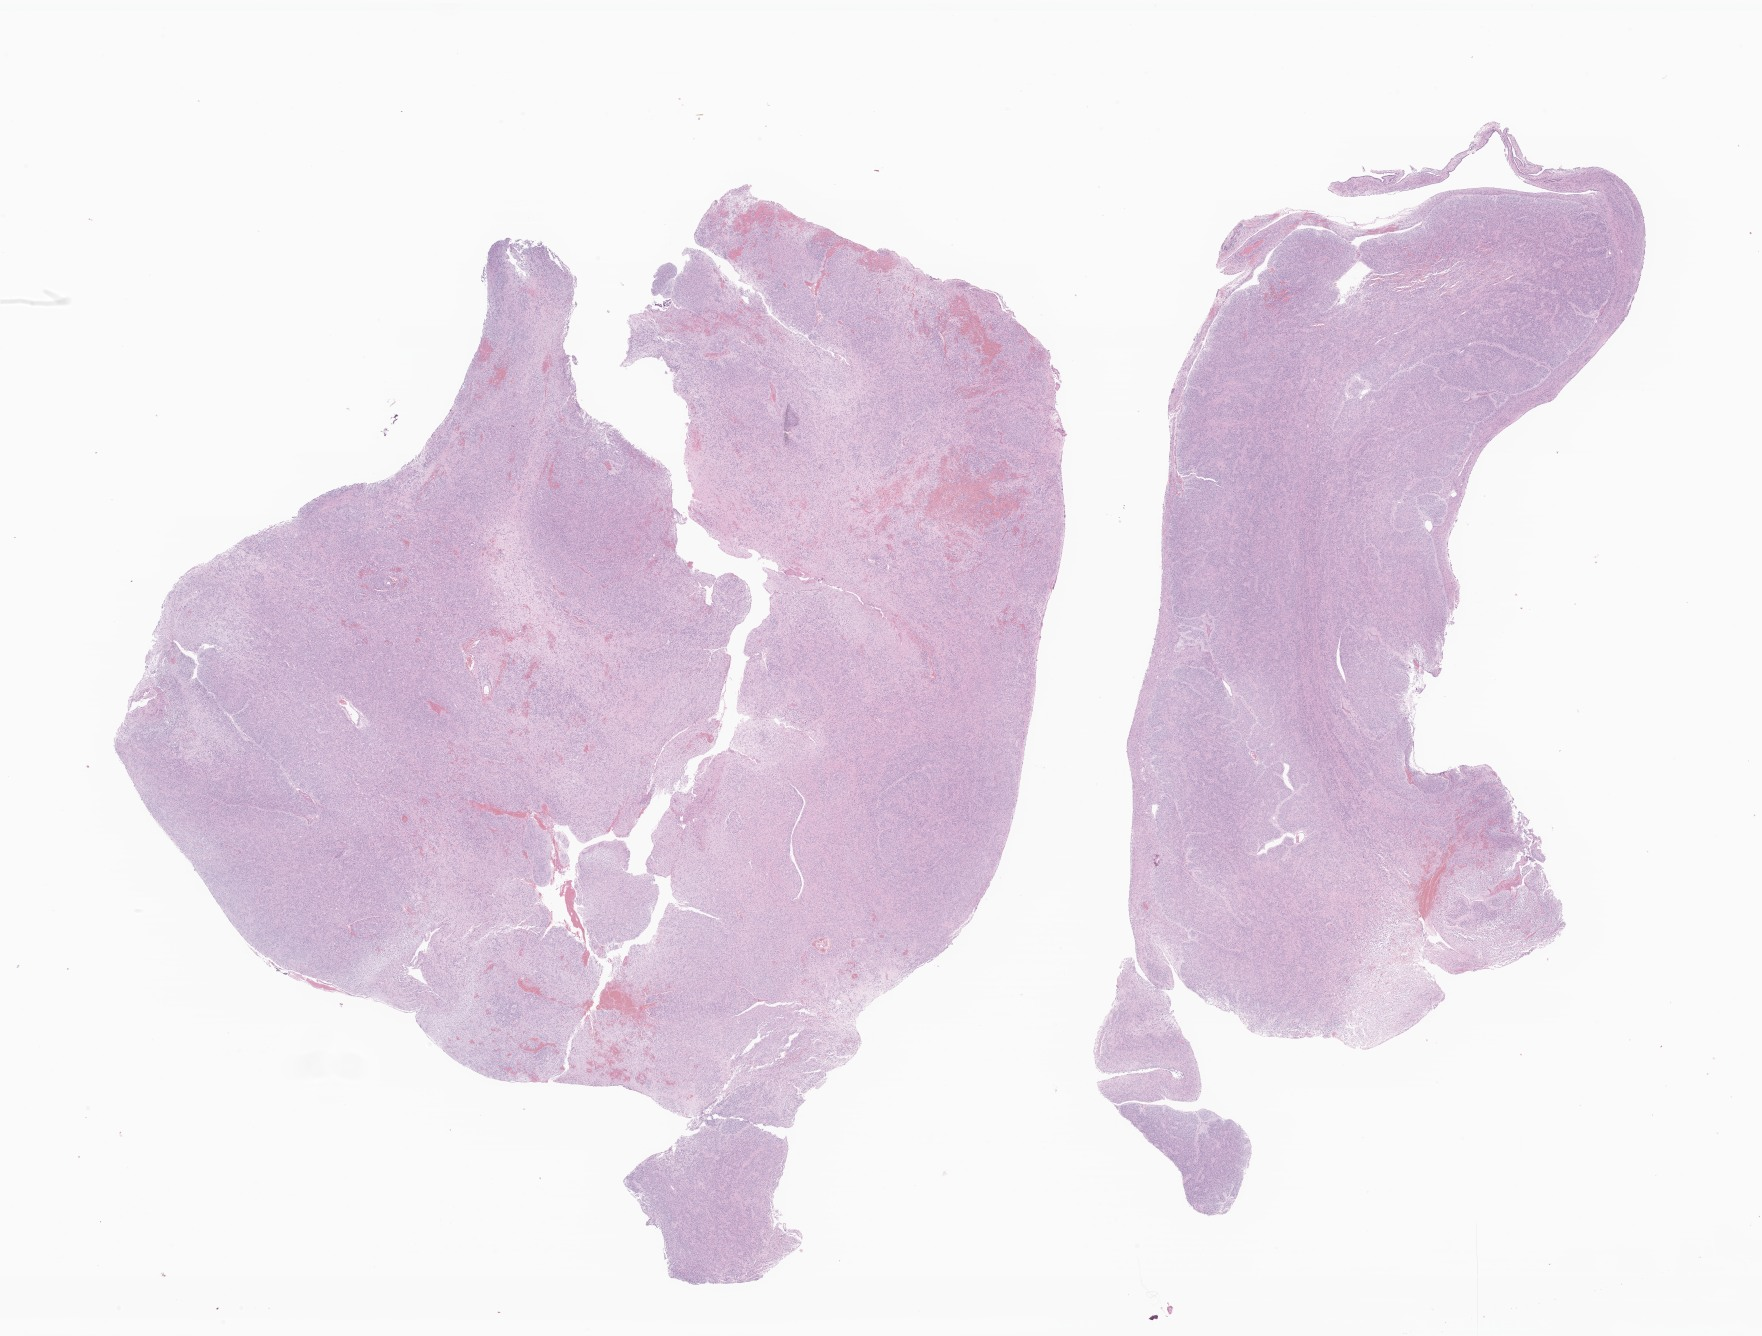
H&E whole-slide image of tumor tissue from the brain, shown as a low-resolution overview of the whole scanned area (about 29.7 x 22.5 mm). FFPE section. Female patient, age 785 days (about 2.1 years).
Recorded diagnosis: Ependymoma, NOS.